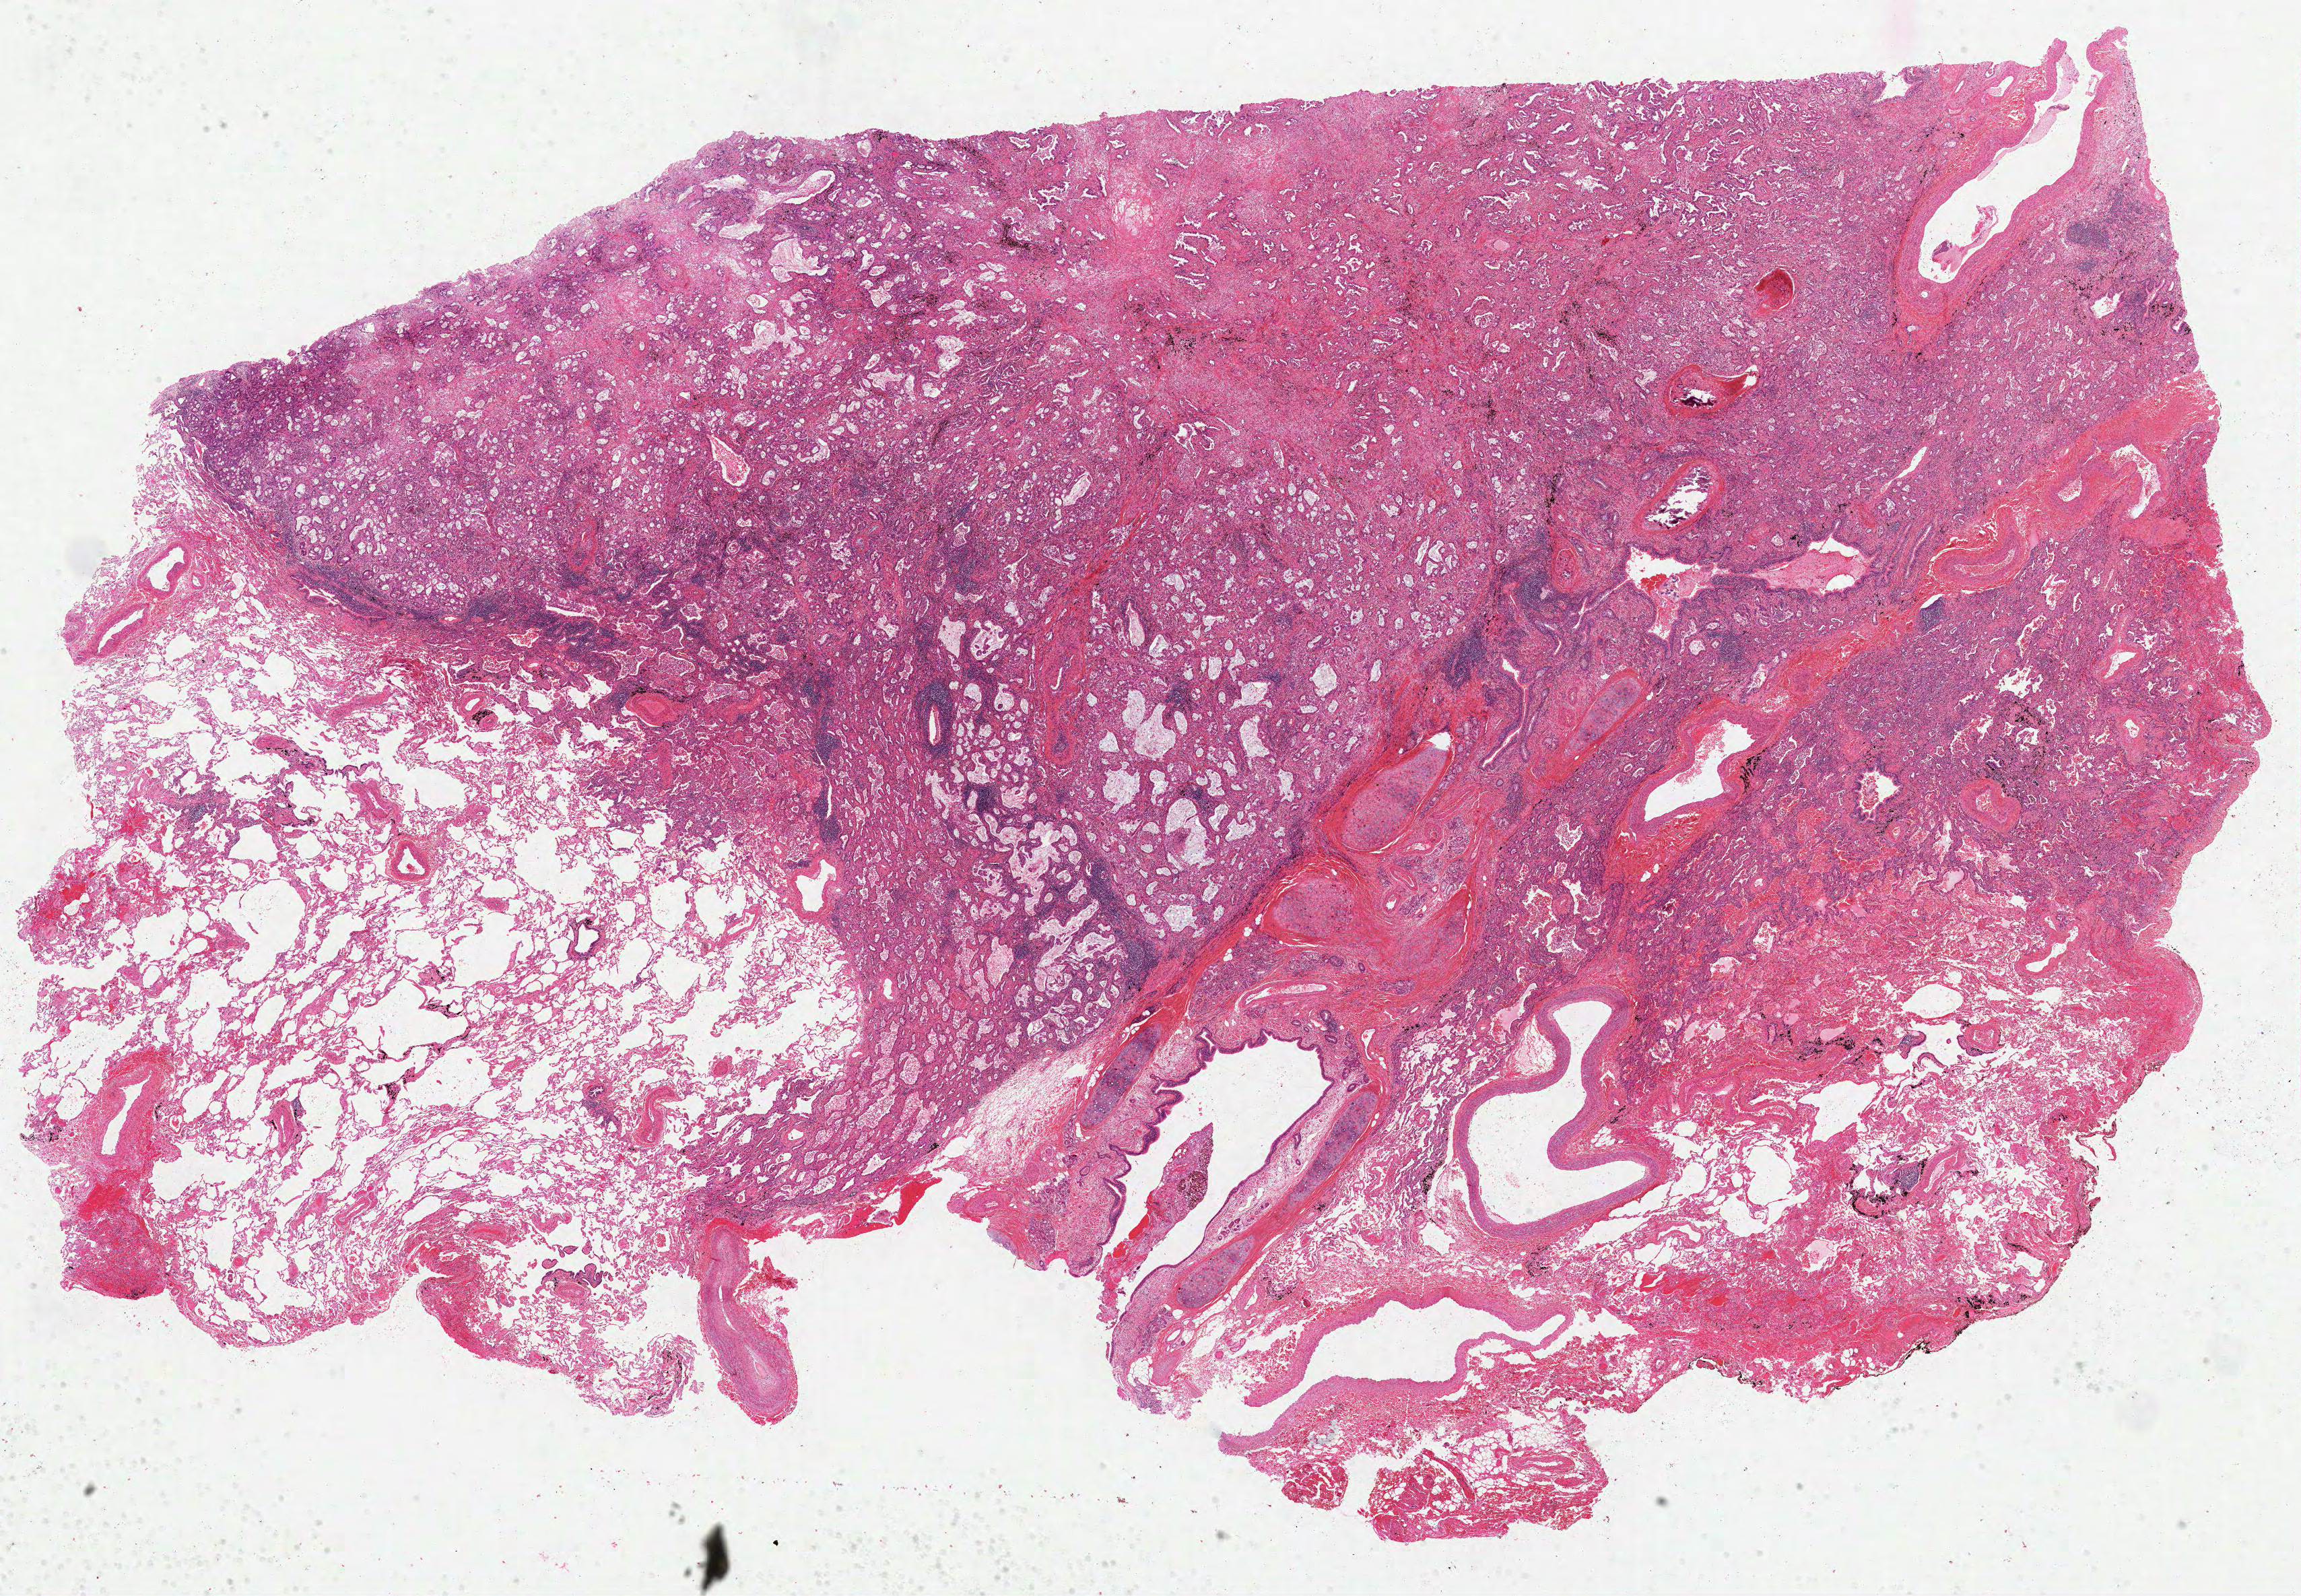
Digitized H&E tissue section (whole slide), shown as a low-resolution overview of the whole scanned area (about 27.6 x 19.1 mm, acquisition: 40x scan); formalin-fixed paraffin-embedded (FFPE) diagnostic section; lung, primary tumour sample. Patient: male, age at initial diagnosis 68 years.
Diagnosis: Squamous cell carcinoma, keratinizing, NOS (lower lobe, lung).